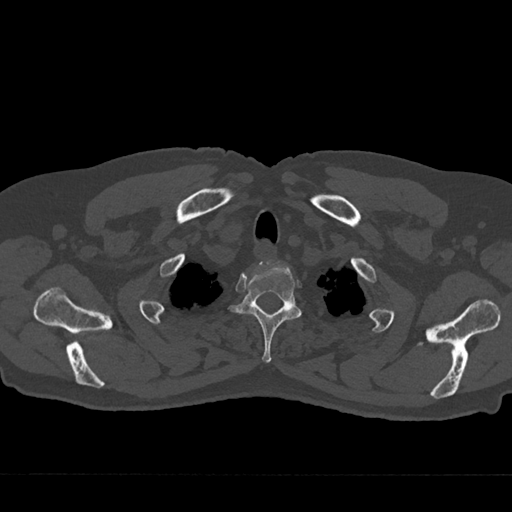
CT including the spine, one axial slice; slice 615 of 797 in the series (ordered by position); 120 kVp; bone window (W 1800 / L 400 HU); 0.5 mm slice thickness; 512 × 512 image matrix, field of view 377 × 377 mm. Male patient, age 75 years. Case-level facts recorded for this patient, not image findings: primary cancer: renal.
Structures marked on this image (semi-automatically segmented with operator editing):
- T2 vertebra: bounding box (x1, y1, x2, y2) in pixels: (229, 261, 302, 363)